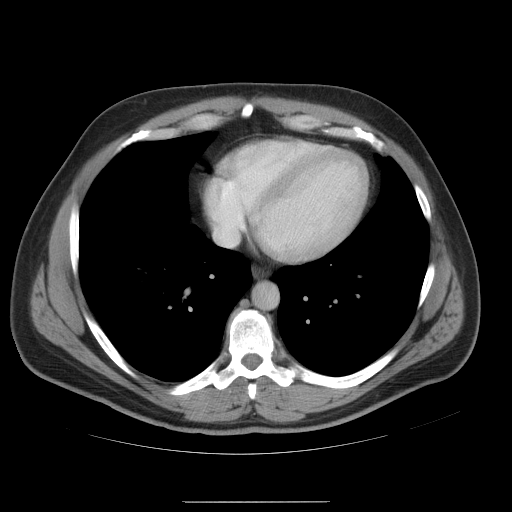
Contrast-enhanced abdominal CT, one axial slice; position 52 of 54 along the scan axis; 120 kVp; intravenous contrast given; soft-tissue window (W 400 / L 40 HU); 5 mm slice thickness; 512 × 512 image matrix, field of view 436 × 436 mm. Male patient, age 40 years. Case-level facts recorded for this patient, not image findings: diagnosis: colorectal cancer liver metastases, imaged before liver resection; multiple liver metastases: no; largest metastasis: 15 cm.
Annotated regions visible in this slice (outlined manually by an expert reader):
- hepatic veins: bounding box [x1, y1, x2, y2] px = [209, 201, 260, 245]